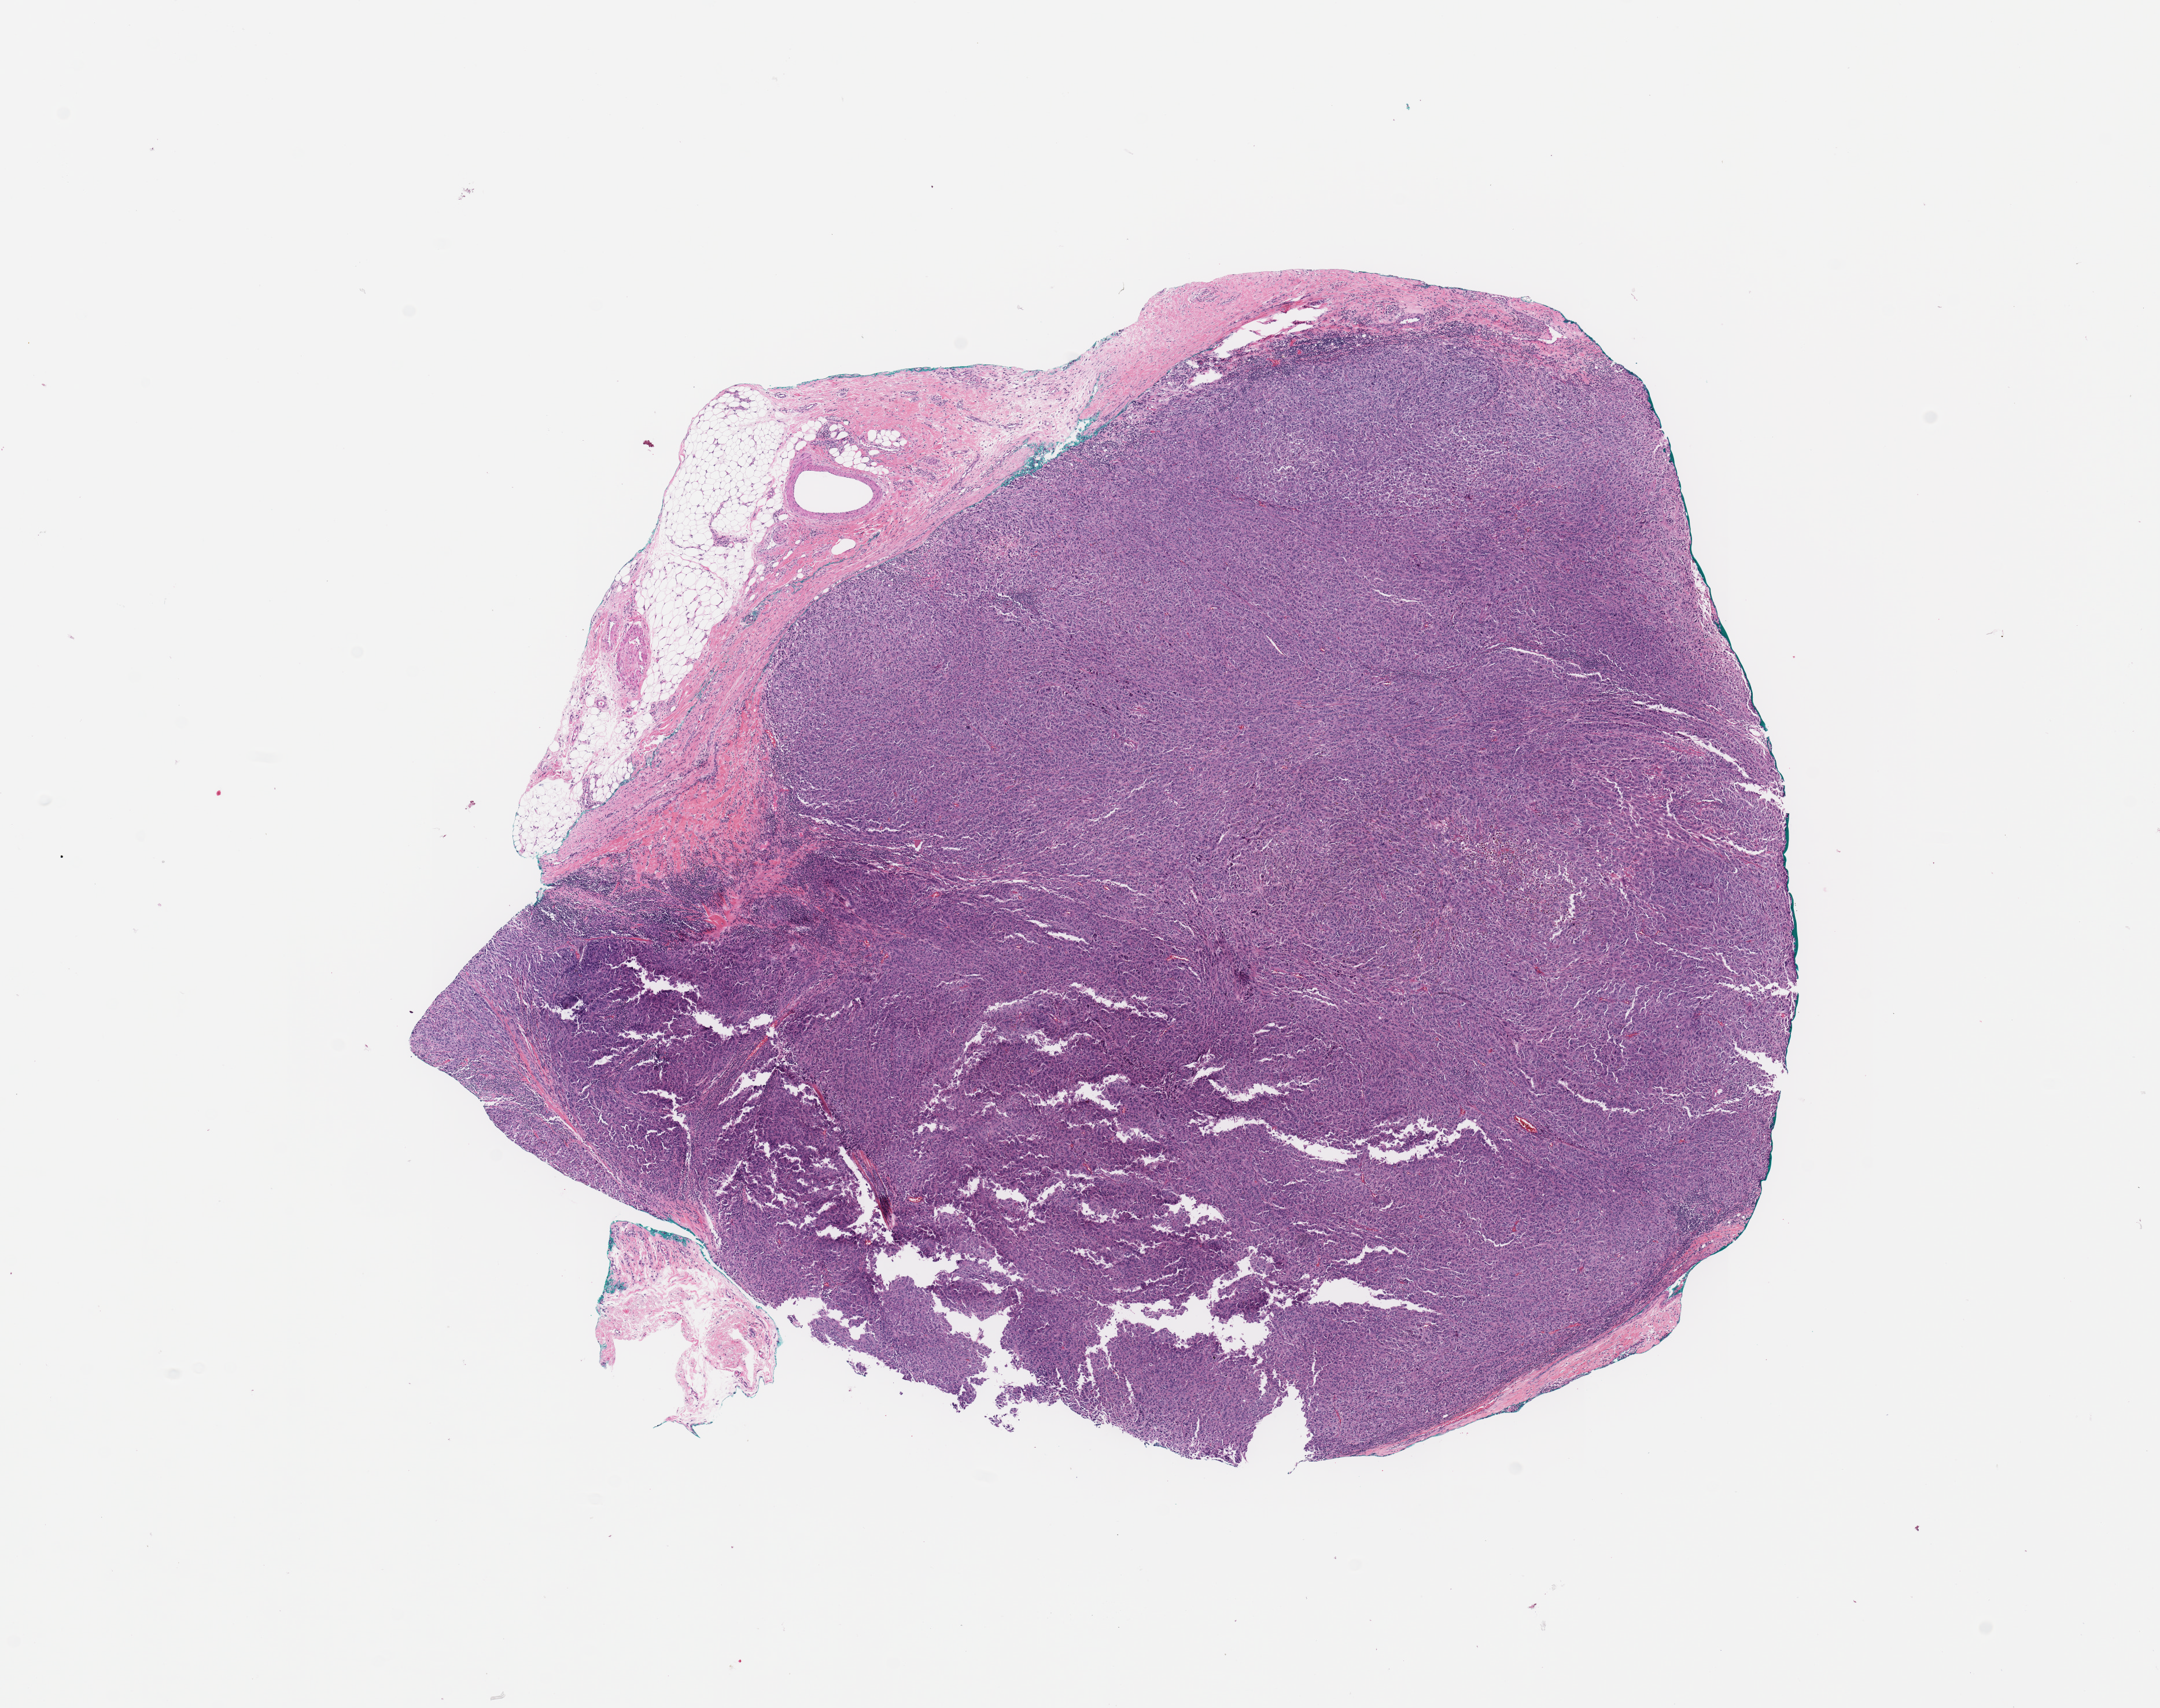
H&E-stained whole-slide image — low-resolution overview of the scanned area, about 14.8 x 11.7 mm. Tumour tissue sample, sampled site: trunk. 83-year-old male patient. Pathologist review of this section (percent, as recorded): tumour nuclei 90%, necrosis 0%.
This section: metastatic tumour tissue. Patient diagnosis: Malignant melanoma, NOS.